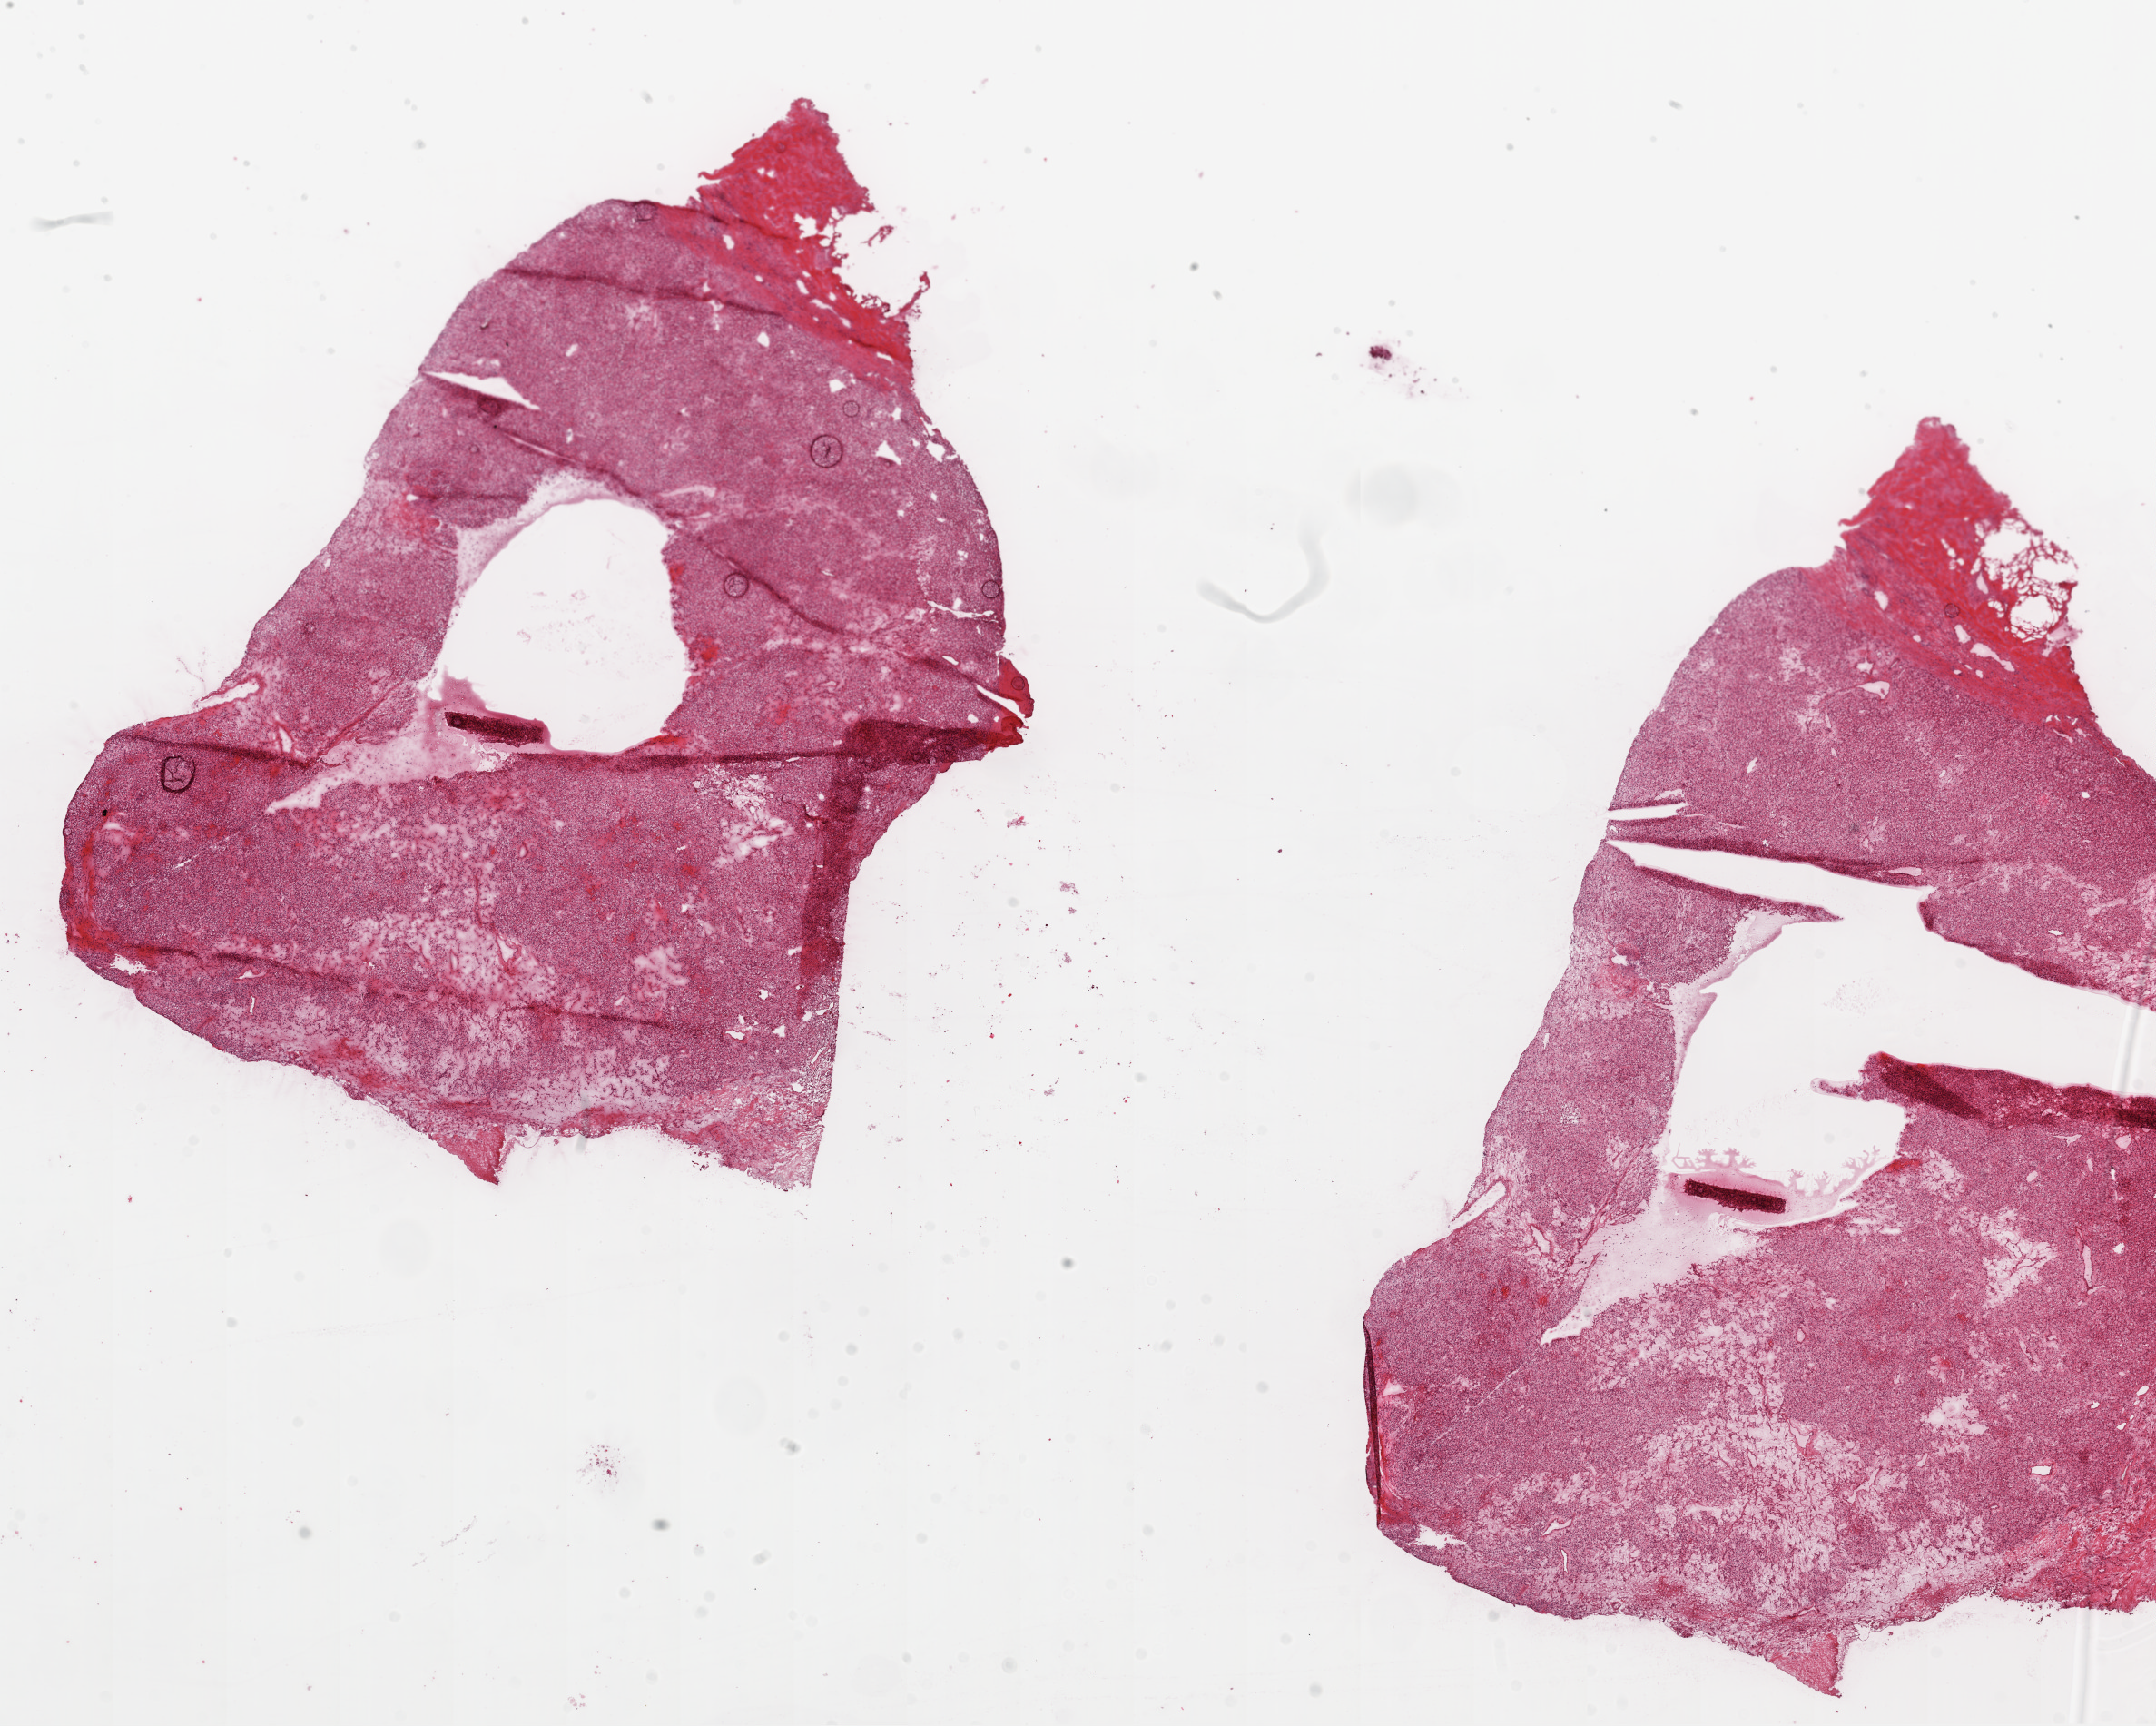
Digitized H&E-stained tissue section (whole slide) — a low-resolution overview of the entire scanned area, about 19.1 x 15.3 mm (acquisition: 20x scan). Frozen section from the top of the tissue portion. Sample: primary tumour, kidney. Male, age 56 years at initial diagnosis. Histologic grade: G2 (moderately differentiated). Pathologist review of this section (percent, as recorded): tumour cells 90%, tumour nuclei 85%, normal cells 0%, stromal cells 10%, necrosis 0%.
• laterality: left
• AJCC pathologic stage: I
• histologic diagnosis: Clear cell adenocarcinoma, NOS